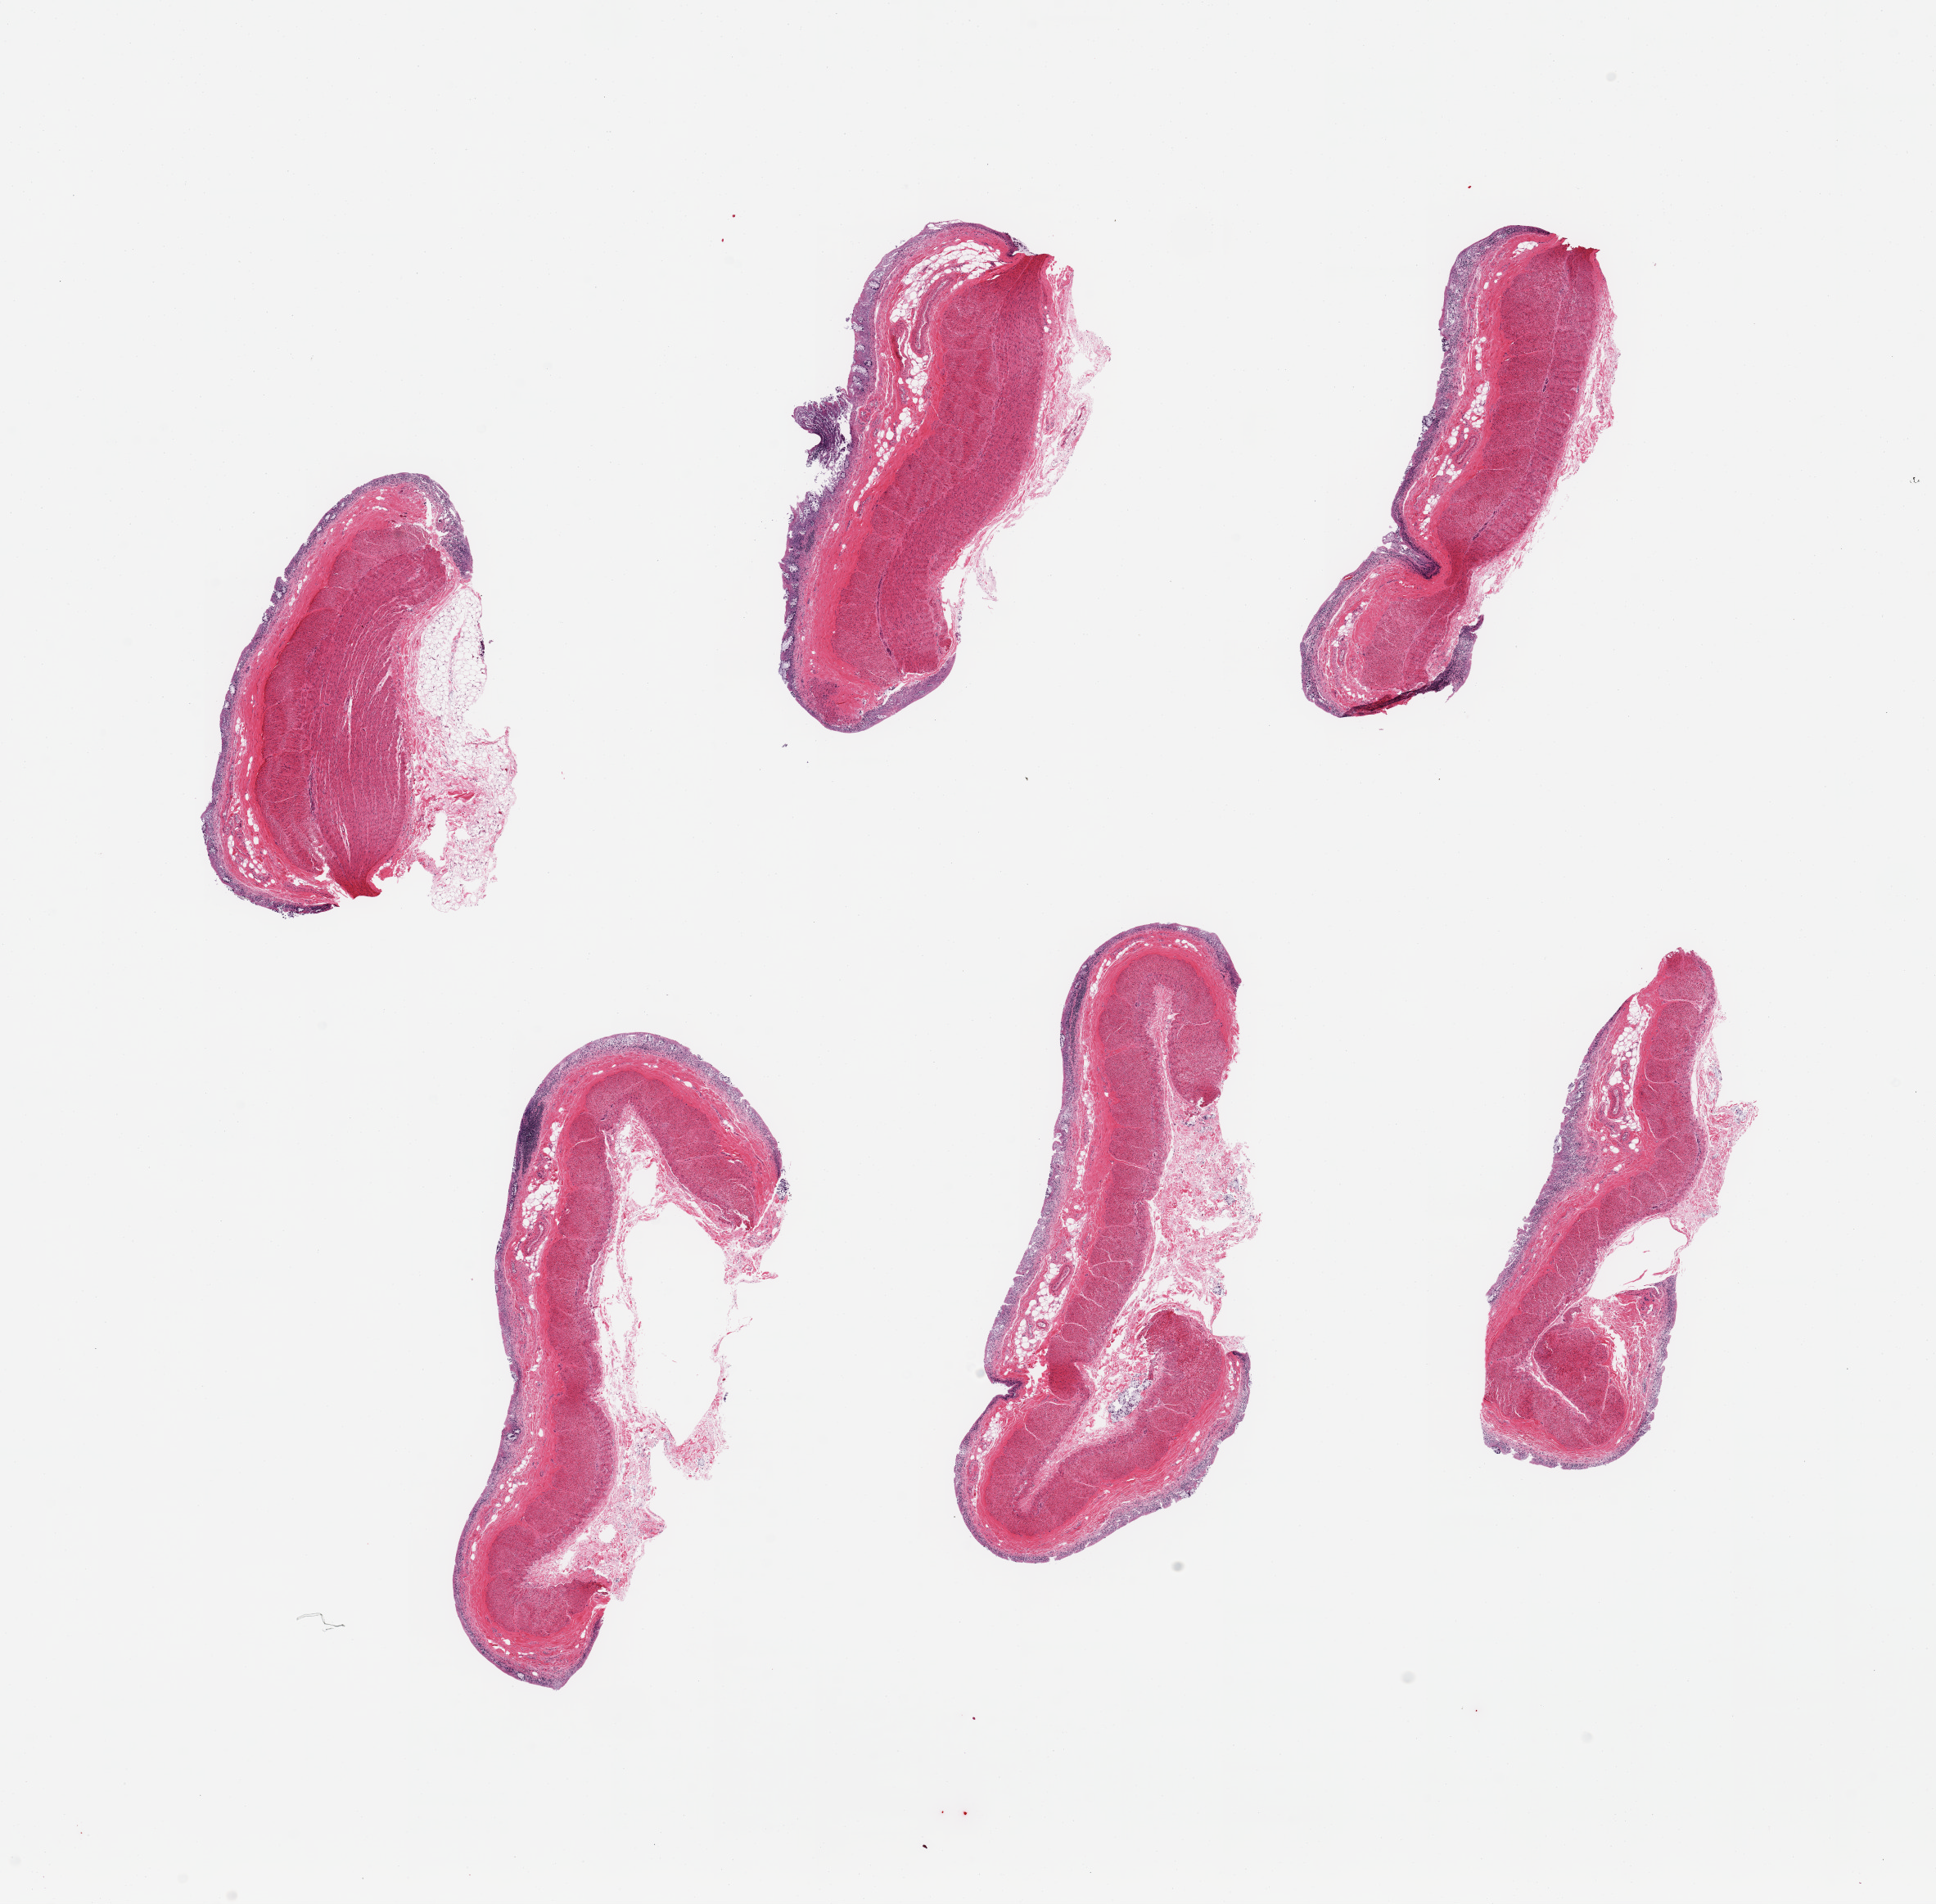
Whole-slide image, haematoxylin and eosin stain — whole scanned area (about 18.7 x 18.4 mm) shown as a low-resolution overview, PAXgene-fixed paraffin-embedded (PFPE) section, section of transverse colon (target tissue), tissue donor sample. Donor: female.
Reviewer comment on this tissue sample: 6 pieces; mucosa autolyzed on all; muscularis intact.